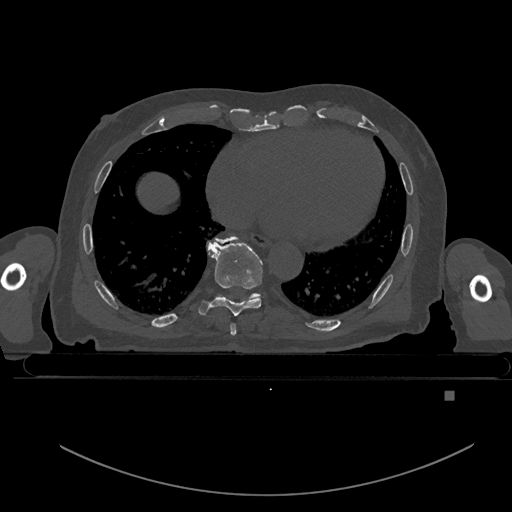
CT including the spine, one axial slice; position 195 of 969 along the scan axis; bone window (W 1800 / L 400 HU); 0.5 mm slice thickness; 512 × 512 image matrix. Patient: male, 82 years. Case-level facts recorded for this patient, not image findings: primary cancer: prostate; vertebrae with lytic lesions (as recorded): T11, T9, T8, T2.
Outlined on this slice (semi-automatically segmented with operator editing):
- T7 vertebra: bounding box <230,323,236,336> (left, top, right, bottom; pixels)
- T8 vertebra: <198,237,263,316>
- T9 vertebra: <215,236,260,300>